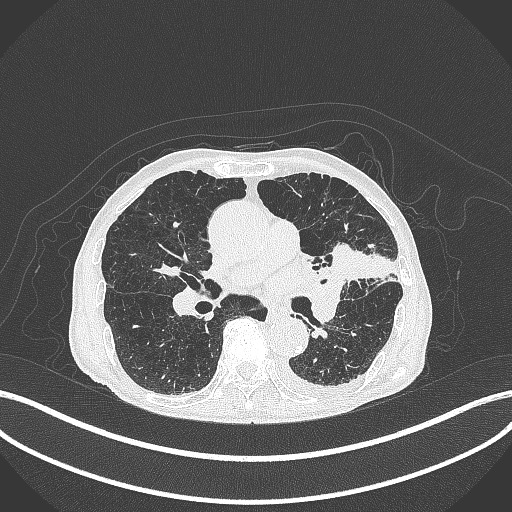
Chest CT, one axial slice. Slice 204 of 385 in the series (ordered by position). Reconstruction kernel B70f. Lung window (W 1500 / L -600 HU). 1 mm slice thickness. 512 × 512 image matrix. Male patient, age 90 years or older. Case-level facts recorded for this patient, not image findings: clinical TNM (as recorded): T2b N1 M0.
Structures marked on this image (bounding box drawn by a radiologist):
- lung tumour (recorded histology: squamous cell carcinoma): bounding box [x1, y1, x2, y2] px = [331, 235, 372, 289]